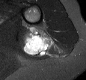
MRI of an extremity soft-tissue mass, one axial slice. Position 9 of 30 along the scan axis. STIR. MR volume resampled by the dataset authors to the PET/CT grid (not the native acquisition matrix). 3.27 mm slice thickness. 86 × 80 image matrix, field of view 84 × 78 mm. Female patient. From the clinical record (not read from this slice): histological type: malignant fibrous histiocytoma; grade: low; site of the primary tumour: left arm.
Outlined on this slice (expert contour drawn on MRI and transferred to this co-registered scan by the dataset authors):
- gross tumour volume (mass): box from (x=22, y=26) to (x=54, y=57) px